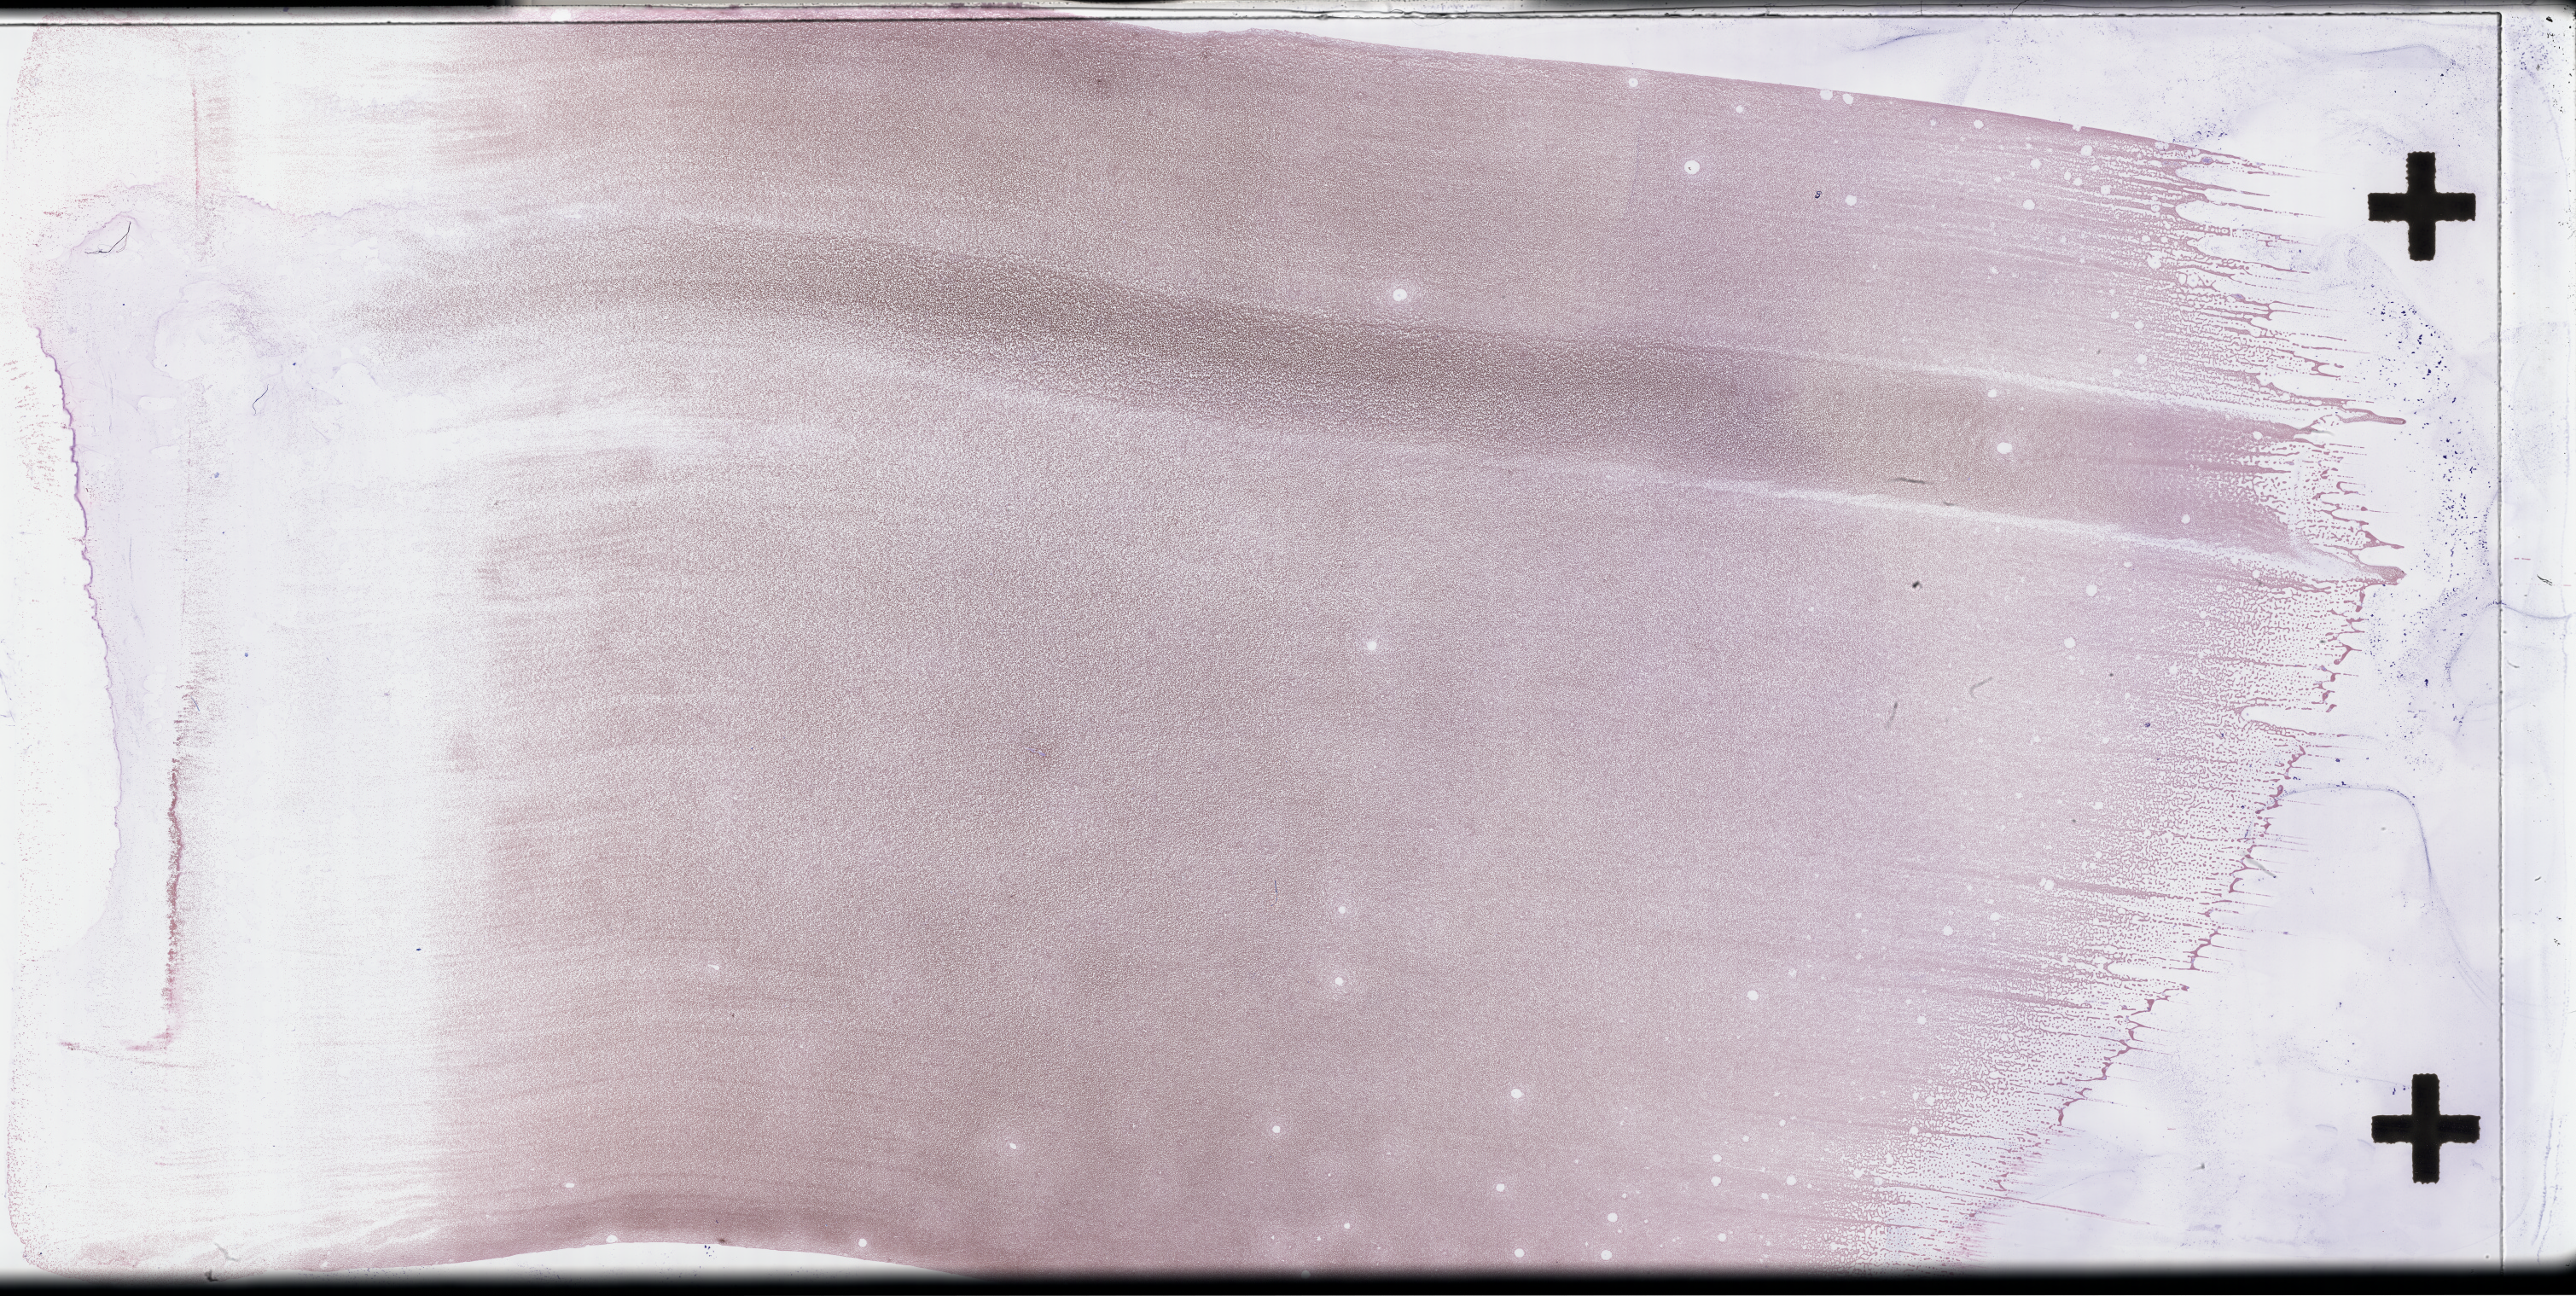
Wright–Giemsa-stained bone marrow smear, whole-slide image — low-resolution overview of the scanned area, about 48.8 x 24.5 mm, collected on treatment. Female patient.
Patient diagnosis: Acute Myeloid Leukemia Not Otherwise Specified.